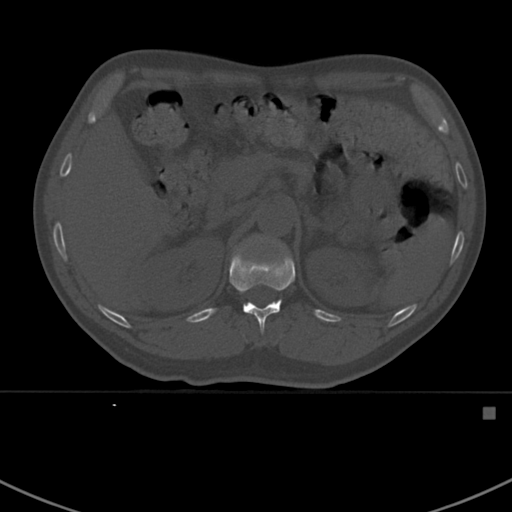
CT including the spine, one axial slice; position 326 of 412 along the scan axis; reconstruction kernel Br40s; bone window (W 1800 / L 400 HU); 1.5 mm slice thickness; 512 × 512 image matrix, field of view 358 × 358 mm. Male patient, age 59 years. Case-level facts recorded for this patient, not image findings: primary cancer: prostate.
Annotated regions visible in this slice (semi-automatic segmentation, software-assisted and operator-edited):
- L1 vertebra: bounding box [x1, y1, x2, y2] px = [268, 240, 270, 242]
- T12 vertebra: [230, 248, 296, 334]